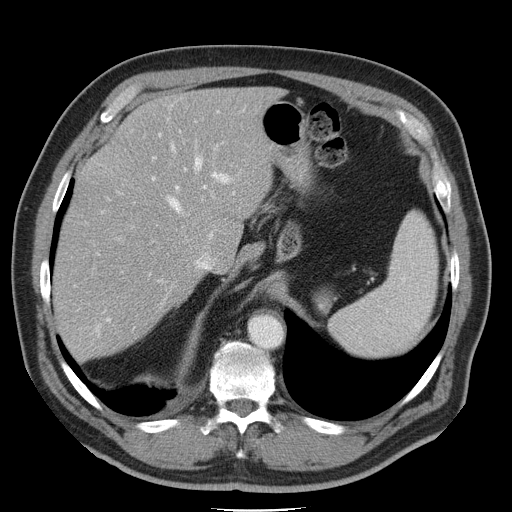
Contrast-enhanced abdominal CT, one axial slice; slice 34 of 45 in the series (ordered by position); 120 kVp; intravenous contrast given; soft-tissue window (W 400 / L 40 HU); 512 × 512 image matrix. Male patient, age 65 years. Case-level facts recorded for this patient, not image findings: diagnosis: colorectal cancer liver metastases, imaged before liver resection.
Annotated regions visible in this slice (expert manual segmentation):
- hepatic veins: bounding box (x1, y1, x2, y2) in pixels: (82, 141, 213, 337)
- liver: (55, 88, 273, 358)
- planned liver remnant (the part of the liver to remain after resection): (104, 88, 273, 262)
- portal vein (with intrahepatic branches): (98, 134, 232, 255)